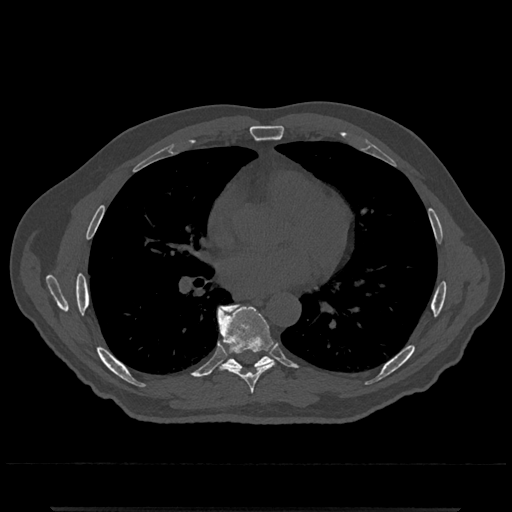
CT including the spine, one axial slice. Slice 701 of 797 in the series (ordered by position). 120 kVp. Bone window (W 1800 / L 400 HU). 0.5 mm slice thickness. 512 × 512 image matrix. Patient: male, 67 years. Case-level facts recorded for this patient, not image findings: primary cancer: prostate.
Structures marked on this image (semi-automatic segmentation, software-assisted and operator-edited):
- T7 vertebra: bounding box (x1, y1, x2, y2) in pixels: (218, 307, 275, 394)
- T8 vertebra: (217, 304, 272, 371)